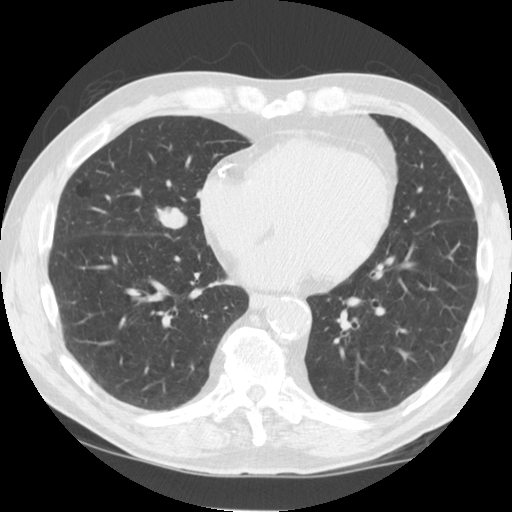
Low-dose screening chest CT, axial slice, third screening round (two years after baseline), lung window (W 1500 / L -600 HU), standard (soft-tissue) reconstruction kernel (STANDARD), 120 kVp, slice 83 of 125 in the series, 512 × 512 image matrix. Male participant, aged 64 years at enrolment.
- Expert reader's lesion annotation, bounding box <134,194,200,248> (left, top, right, bottom; pixels).
- The exam's reader record, not a measurement of the box and not confirmed to be the same lesion: non-calcified nodule or mass ≥4 mm, right middle lobe, 21 × 14 mm, smooth margins, soft tissue attenuation, pre-existing on the prior screen: yes; interval growth: yes.
- Official screen result: positive, other.
- Lung cancer was diagnosed 74 days after this screen: non-small cell carcinoma, right middle lobe, poorly differentiated (G3), stage IIIA (AJCC 6th edition), 20 mm at pathology.